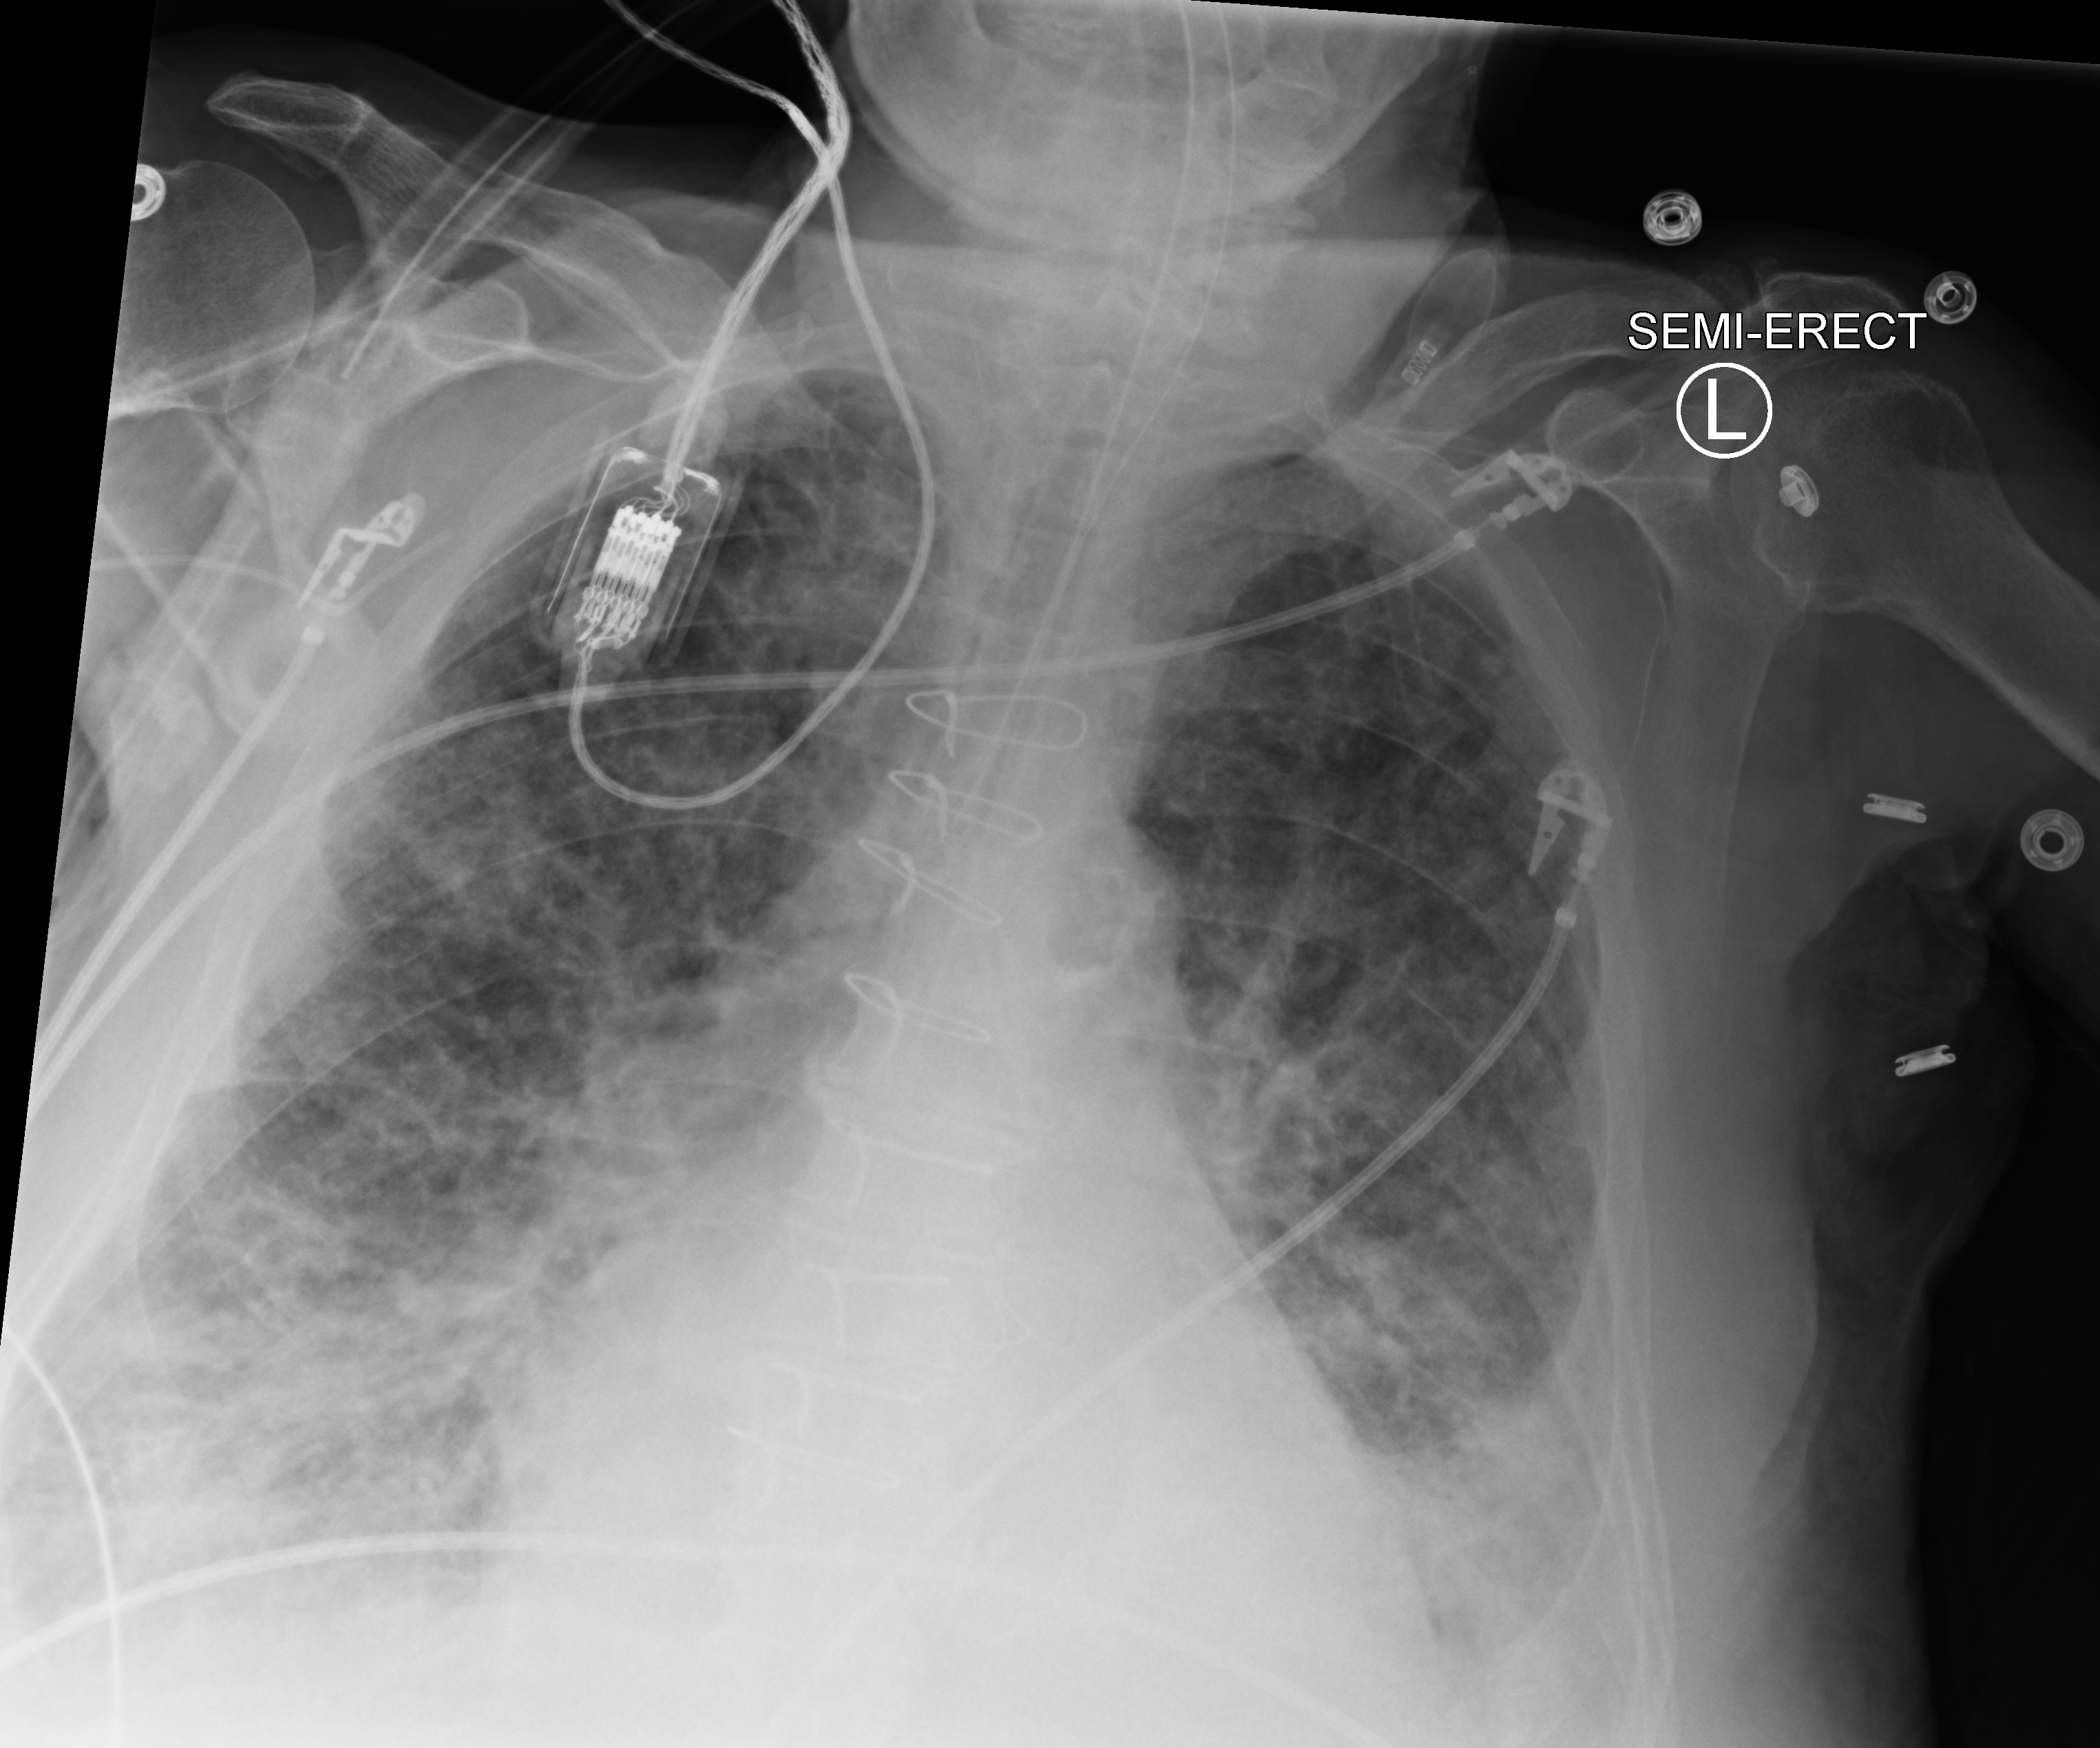
Portable chest radiograph, anteroposterior (AP) projection. Patient hospitalised with COVID-19; male, aged 75–90 years.
Hospital-stay facts (about this admission, not read from this image; timing relative to this image not recorded): length of hospital stay: 40 days; mechanically ventilated during this hospital stay: yes.